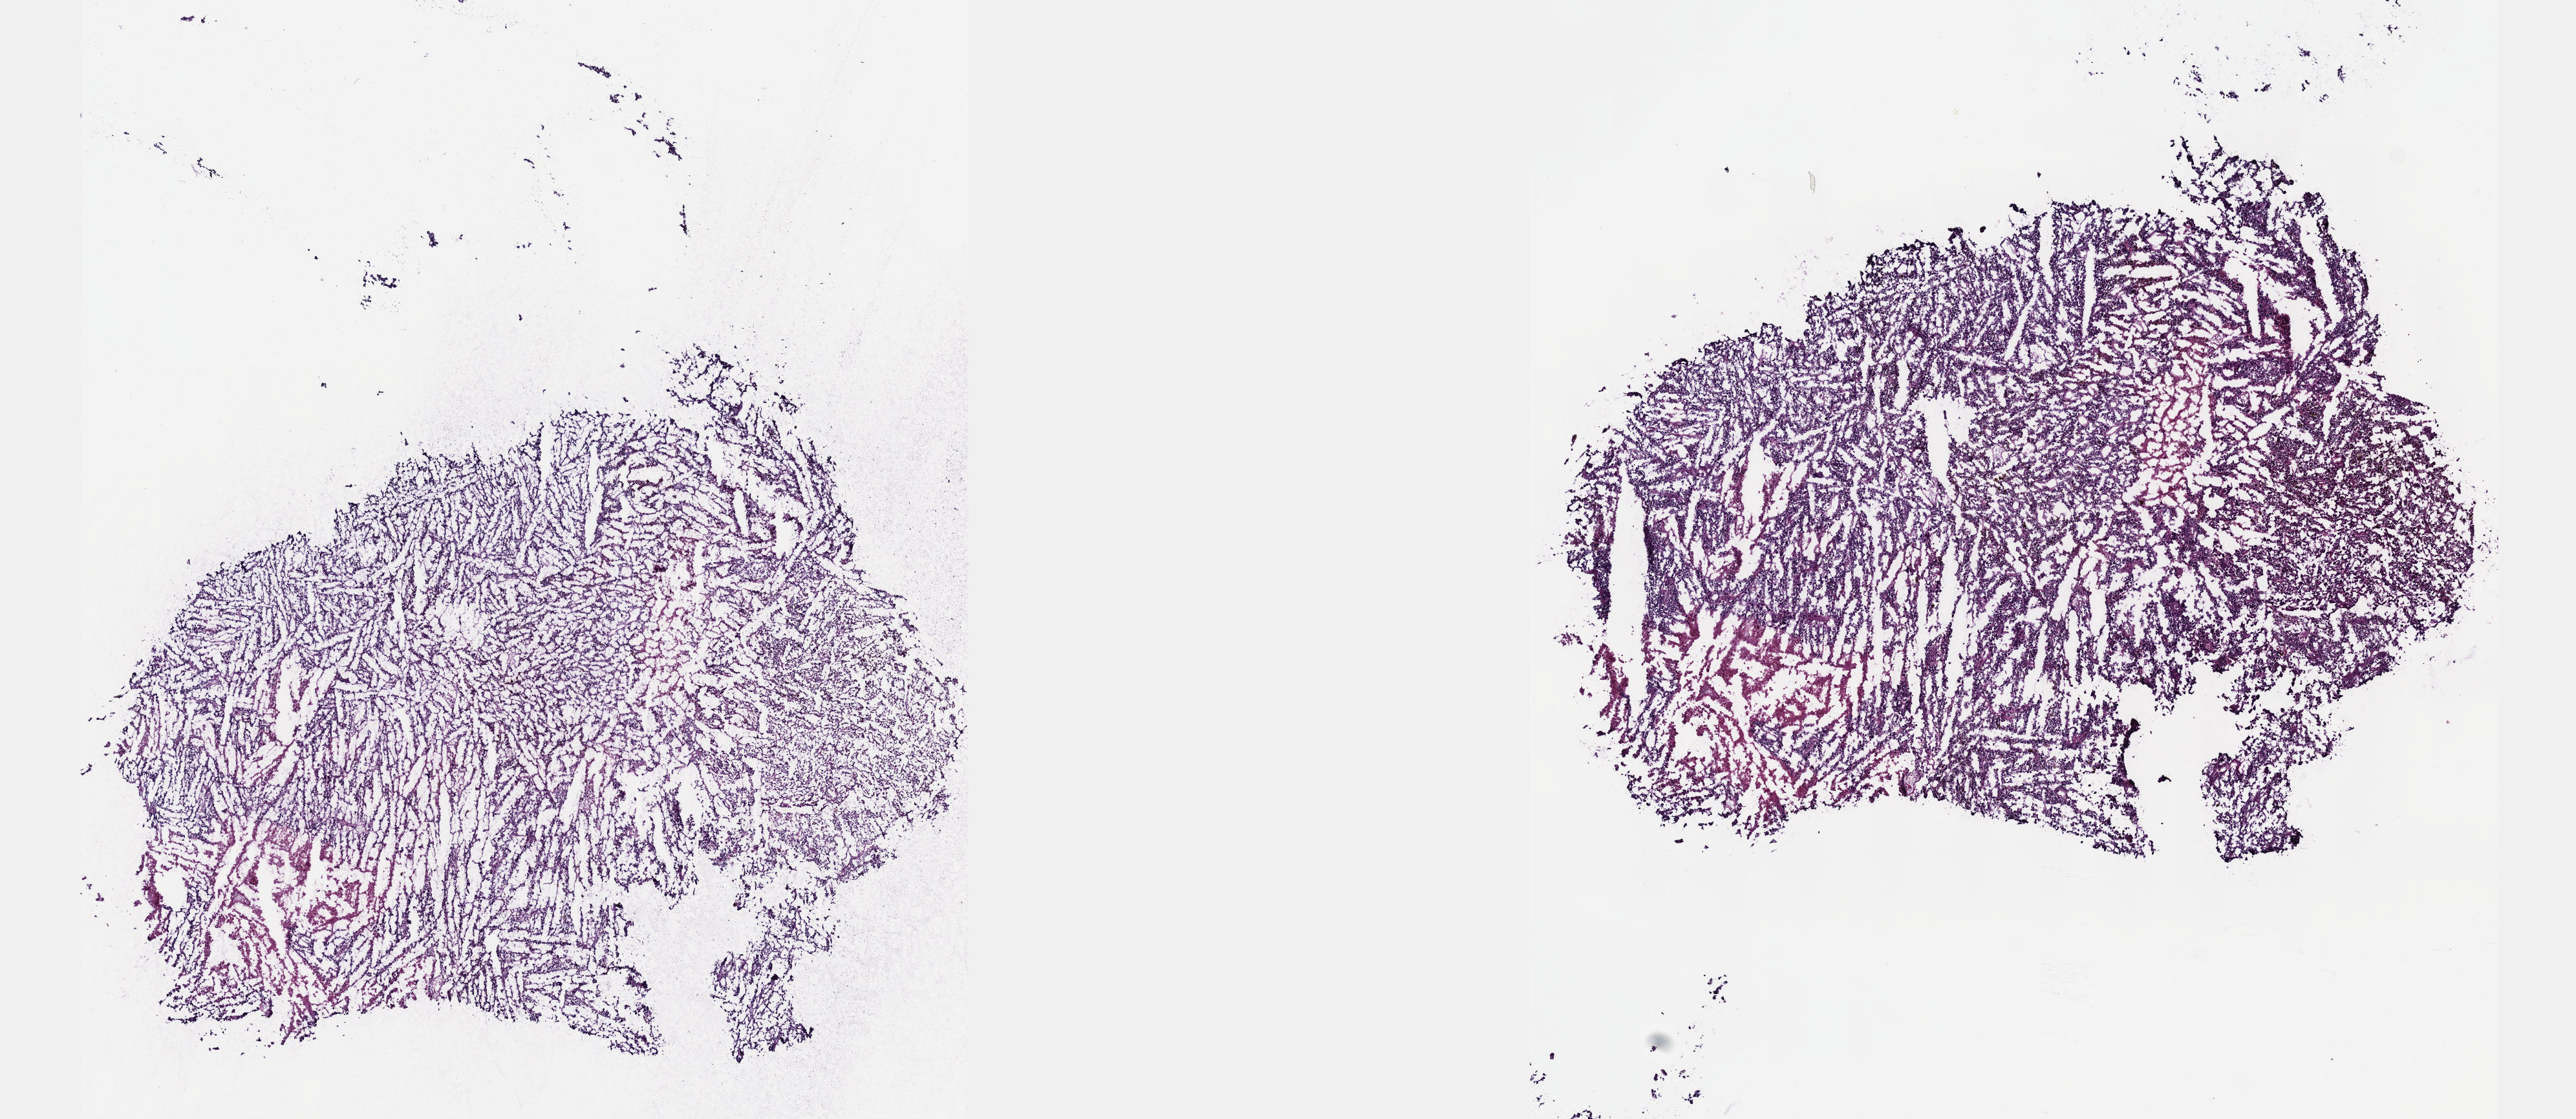
H&E-stained whole-slide image — a low-resolution overview of the entire scanned area, about 16.1 x 7.0 mm (acquisition: 40x scan). Frozen section. Metastatic tumour sample, sampled site not recorded. Male, age 70 years at initial diagnosis. Pathologist review of this section (percent, as recorded): tumour cells 85%, tumour nuclei 95%.
This section: metastatic tumour tissue. Patient diagnosis: Malignant melanoma, NOS.